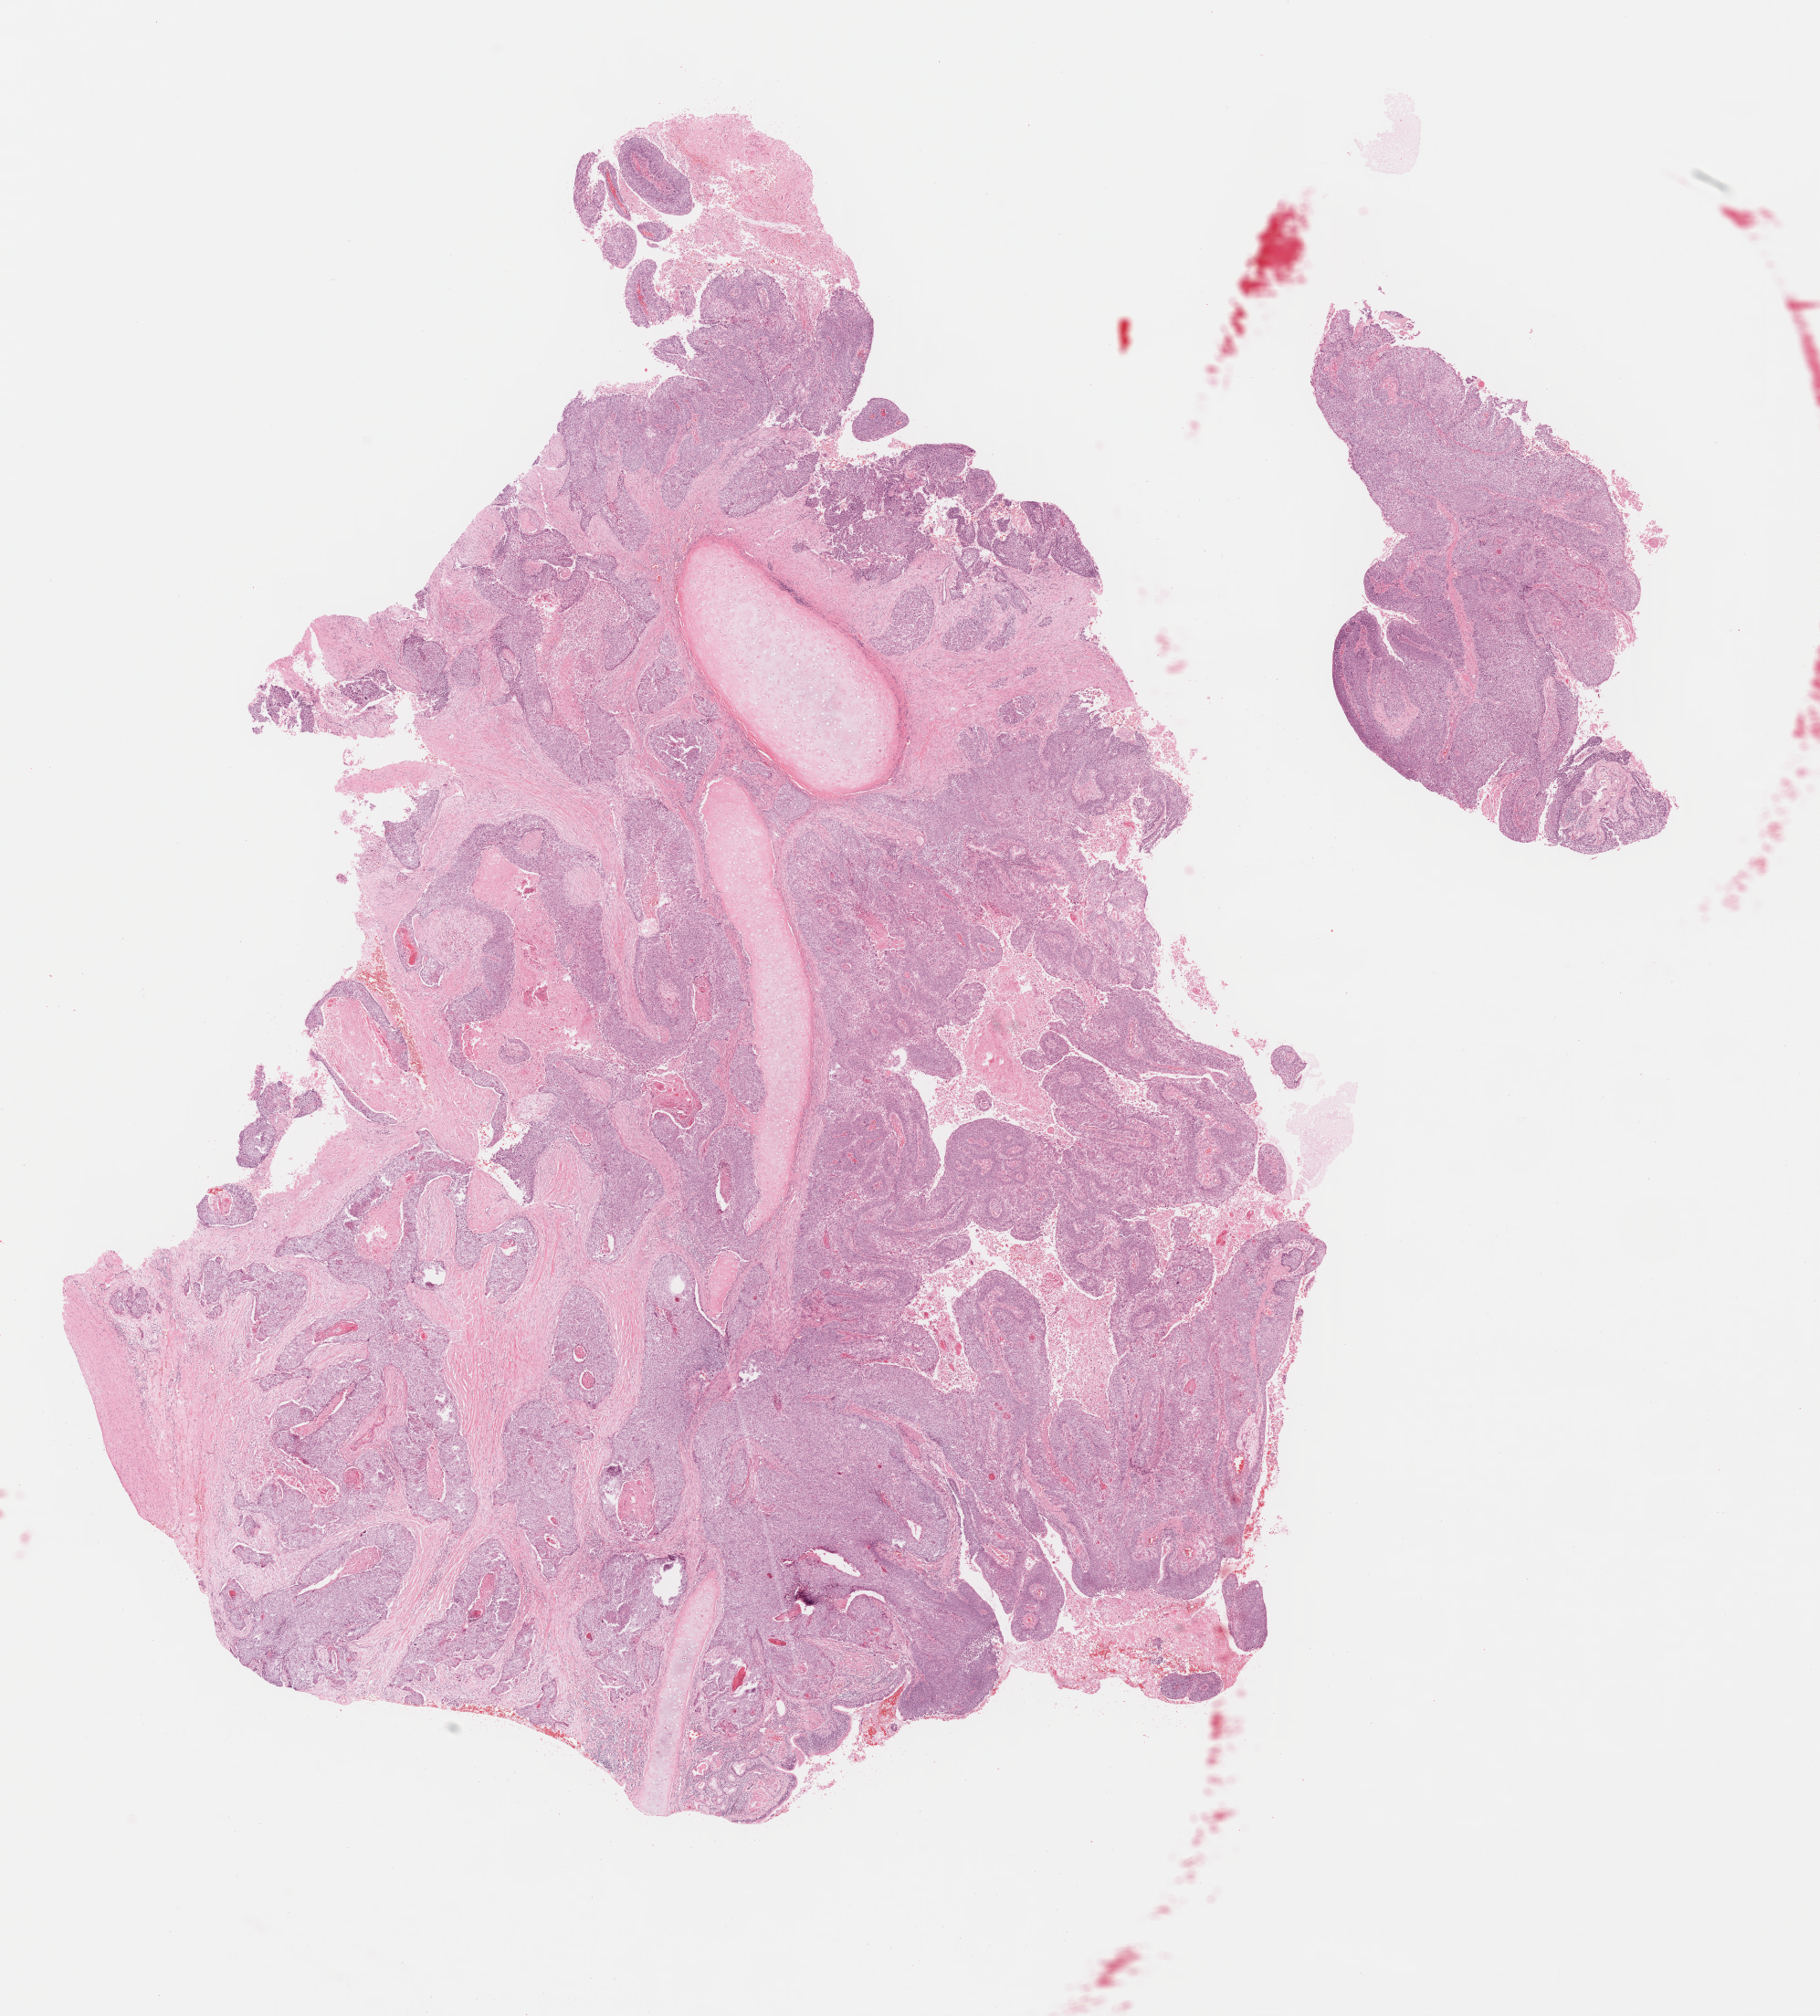
Whole-slide histology image, Hematoxylin and eosin (H&E) stained, a low-resolution overview of the entire scanned area, about 15.7 x 17.4 mm; formalin-fixed paraffin-embedded (FFPE) diagnostic section; primary tumour sample from the lung. Male, age 46 years at initial diagnosis.
- AJCC pathologic stage: IIA (7th edition)
- TNM: T1b N1 M0
- histologic diagnosis: Squamous cell carcinoma, NOS (lower lobe, lung)